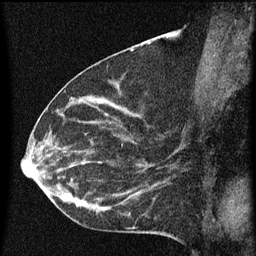
Breast MRI (dynamic contrast-enhanced), one sagittal slice. Slice 30 of 60 in the series (ordered by position). Dynamic contrast-enhanced series, image 2 of 3 at this slice position (ordered by acquisition). 1.5 T. TE 4.2 ms, TR 8 ms. 256 × 256 image matrix, field of view 180 × 180 mm. Female patient, age 55 years.
Annotated regions visible in this slice (semi-automatically segmented with operator editing):
- analysis volume of interest (the breast-tissue region the enhancement analysis was run in; not a lesion): bounding box <51,156,145,217> (left, top, right, bottom; pixels)
- tumour enhancement mask (voxels above the 70 % enhancement threshold inside the analysis volume of interest): <51,160,141,213>